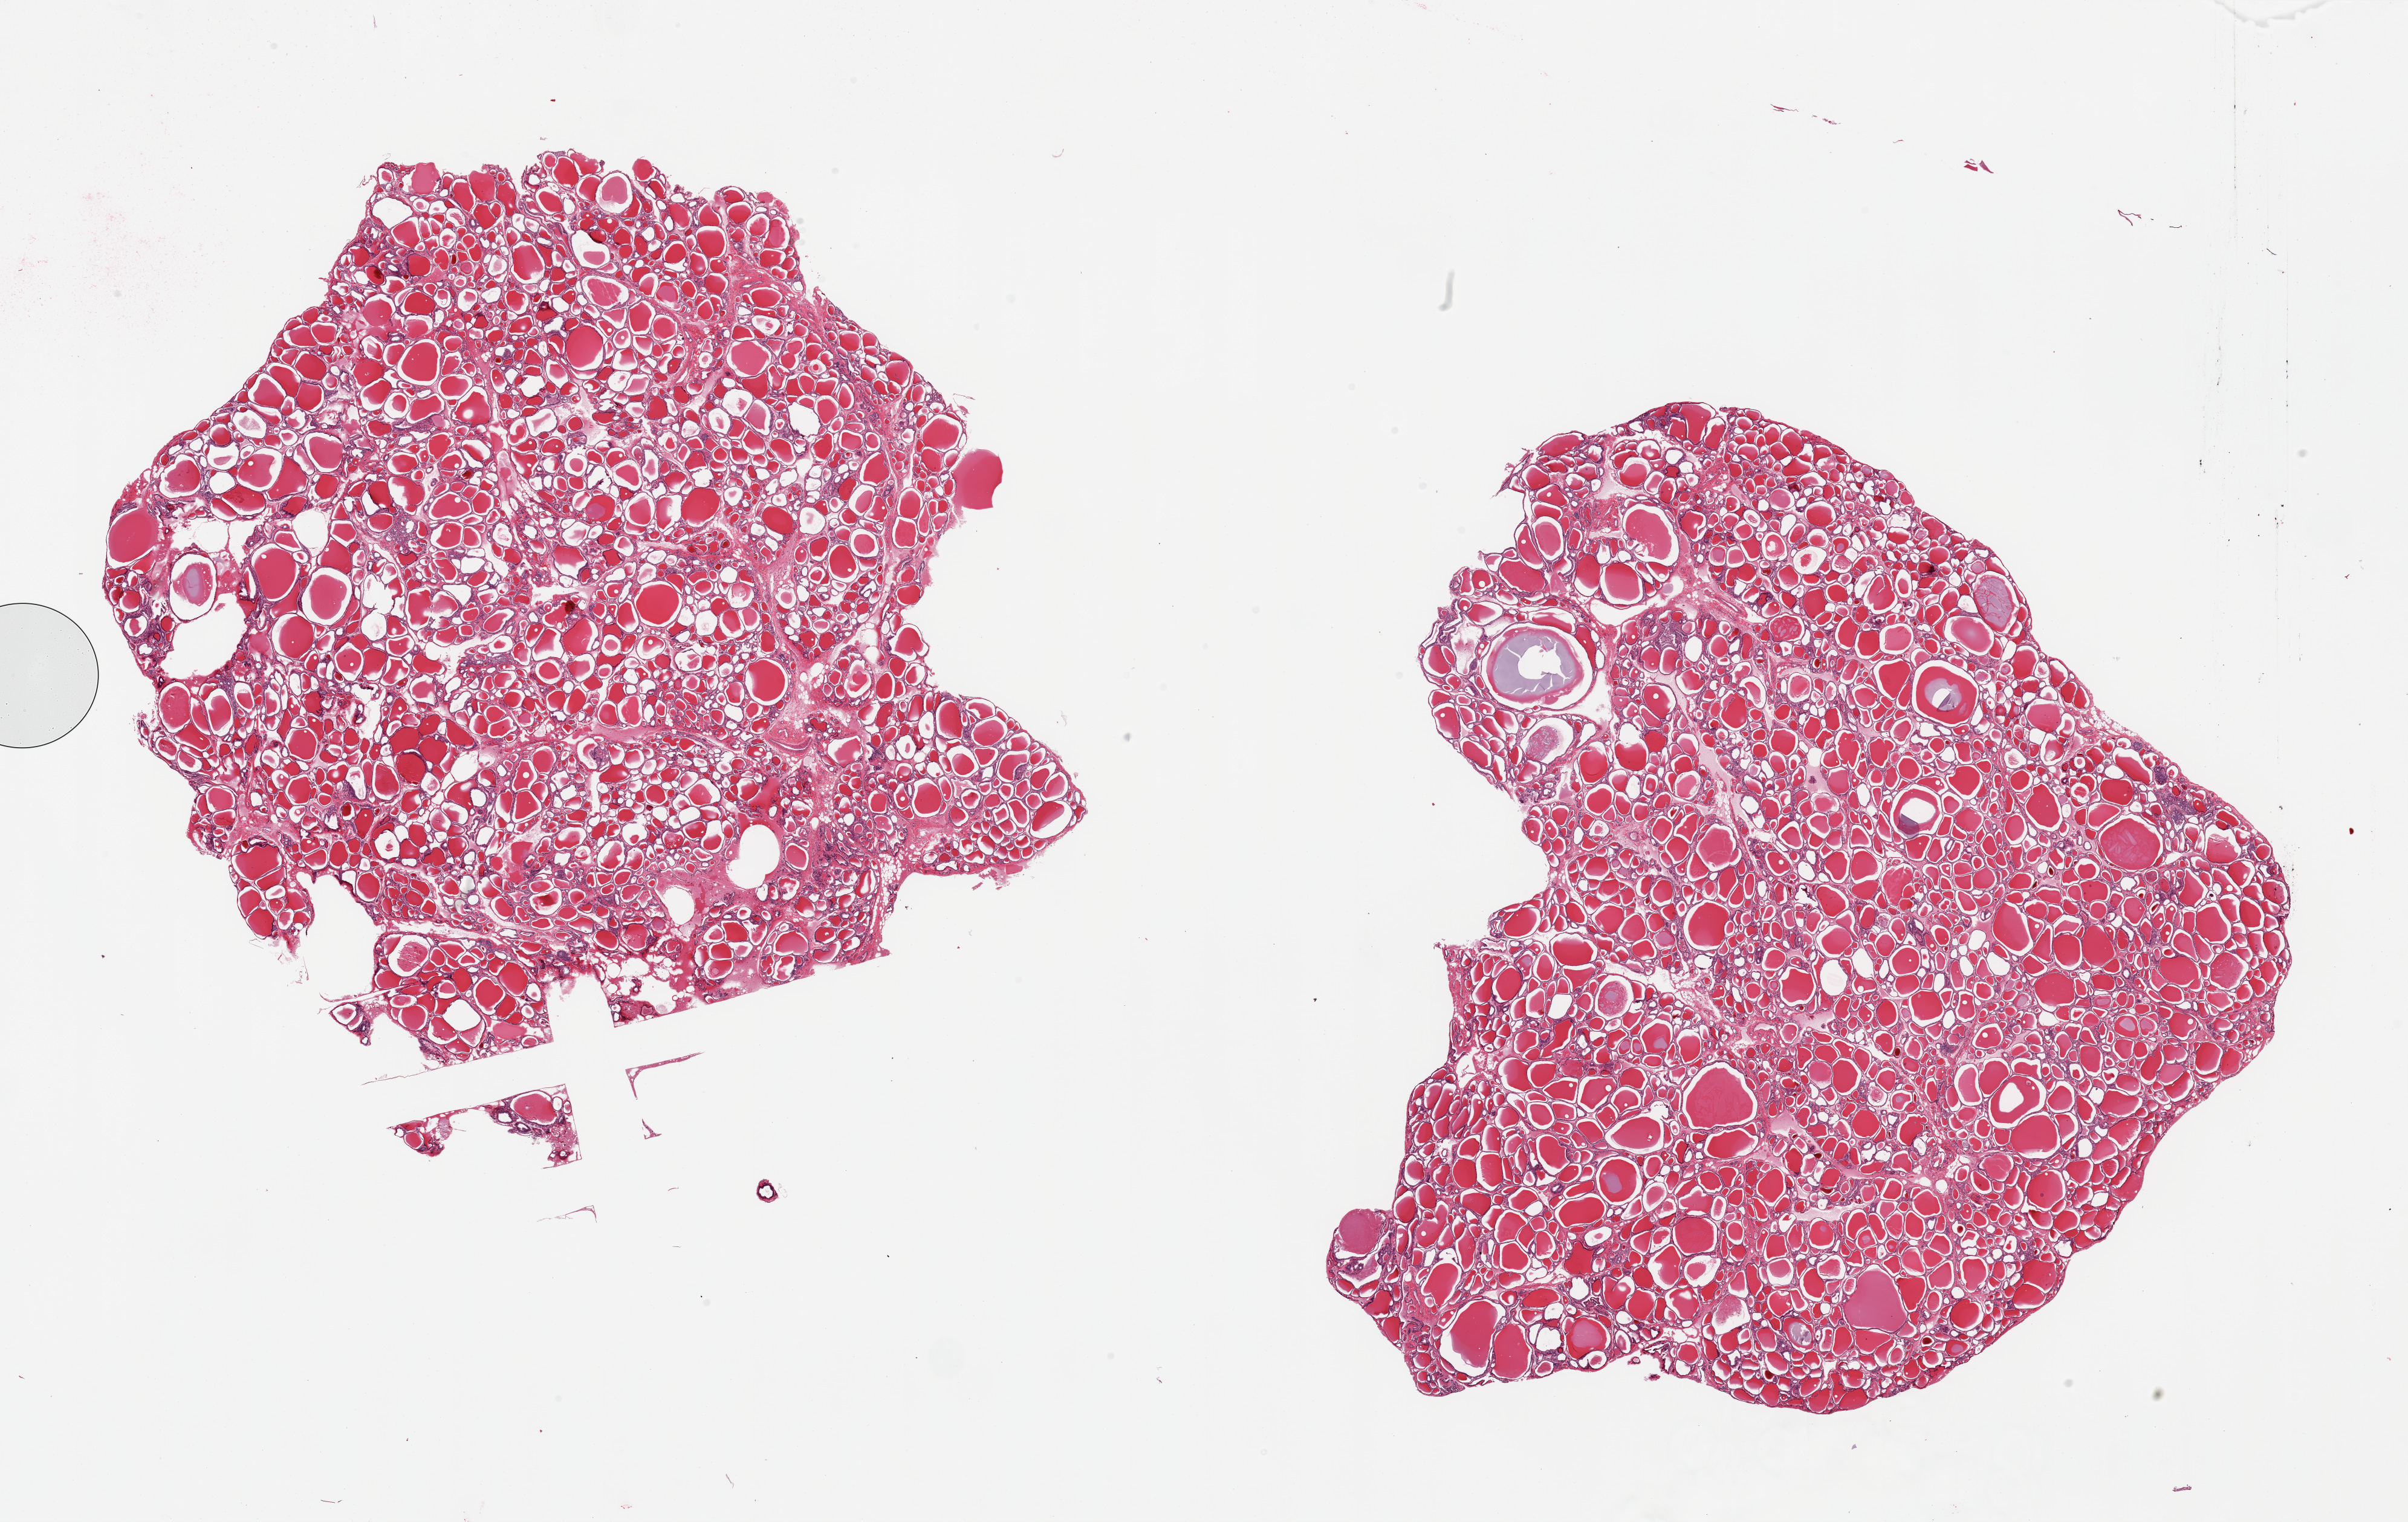
Haematoxylin and eosin whole-slide image, low-resolution overview of the scanned area, about 31.5 x 19.9 mm; PAXgene-fixed, paraffin-embedded tissue; target tissue: thyroid; tissue donor sample. Donor: male.
• pathologist's review note for this sample: 2 pieces